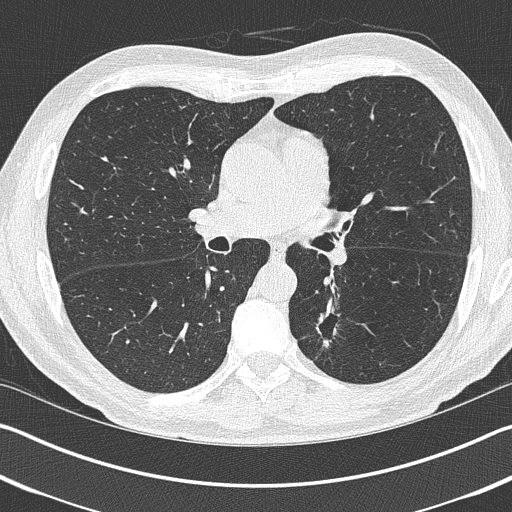
Axial slice from a low-dose chest CT screening exam, baseline screening round, lung window (W 1500 / L -600 HU), 1 mm slice thickness, 120 kVp, 512 × 512 image matrix. Male participant, aged 69 years at enrolment.
Expert-annotated lung lesion, box from (x=298, y=307) to (x=354, y=362) px. Reader record for this screening exam (exam-level; its link to the box is not recorded): non-calcified nodule or mass ≥4 mm, left upper lobe, 19 × 19 mm, spiculated (stellate) margins, pre-existing on the prior screen: yes. Later outcome: lung cancer diagnosed 202 days after this screen — non-small cell carcinoma, left lower lobe, stage IIIA (AJCC 6th edition), 20 mm at pathology.